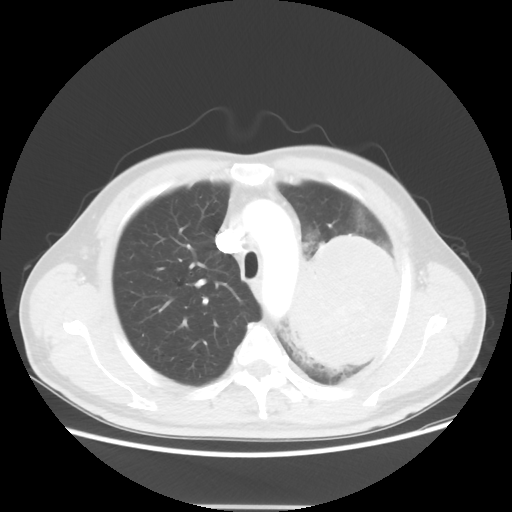
Chest CT, one axial slice. Position 41 of 53 along the scan axis. Reconstruction kernel STANDARD. Lung window (W 1500 / L -600 HU). 512 × 512 image matrix, field of view 391 × 391 mm. Patient: male, 60 years. Case-level facts recorded for this patient, not image findings: clinical TNM (as recorded): T4 N1 M1a; histopathological grade: G3.
Structures marked on this image (rectangle marked by the reading radiologist):
- lung tumour (recorded histology: large cell carcinoma): bounding box [x1, y1, x2, y2] px = [286, 221, 410, 384]